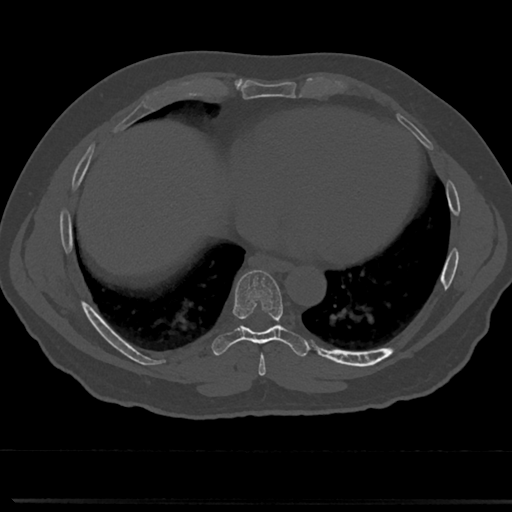
CT including the spine, one axial slice. Reconstruction kernel Br40s/3. 120 kVp. Bone window (W 1800 / L 400 HU). 0.5 mm slice thickness. 512 × 512 image matrix. Male patient, age 61 years. Case-level facts recorded for this patient, not image findings: primary cancer: prostate.
Outlined on this slice (semi-automatically segmented with operator editing):
- T7 vertebra: bounding box <239,329,284,362> (left, top, right, bottom; pixels)
- T8 vertebra: <237,270,283,336>